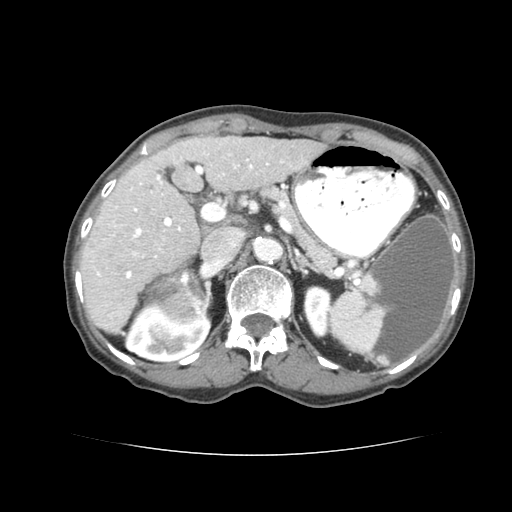
Contrast-enhanced abdominal CT (liver protocol), one axial slice. Position 43 of 77 along the scan axis. Reconstruction kernel STANDARD. 120 kVp. Soft-tissue window (W 400 / L 40 HU). 2.5 mm slice thickness. 512 × 512 image matrix, field of view 340 × 340 mm. From the clinical record (not read from this slice): diagnosis: hepatocellular carcinoma (patient treated with transarterial chemoembolisation; whether this scan precedes or follows treatment is not stated here); TNM stage (as recorded): Stage-I; Child-Pugh class: A; tumour differentiation: well differentiated.
Structures marked on this image (semi-automatically segmented with operator editing):
- liver parenchyma outside the tumour (the mass and vessels are separate outlines, so this box may not span the whole liver): box from (x=78, y=138) to (x=323, y=332) px
- mass: (x=159, y=270)–(x=202, y=322)
- liver vessels: (x=104, y=146)–(x=286, y=274)